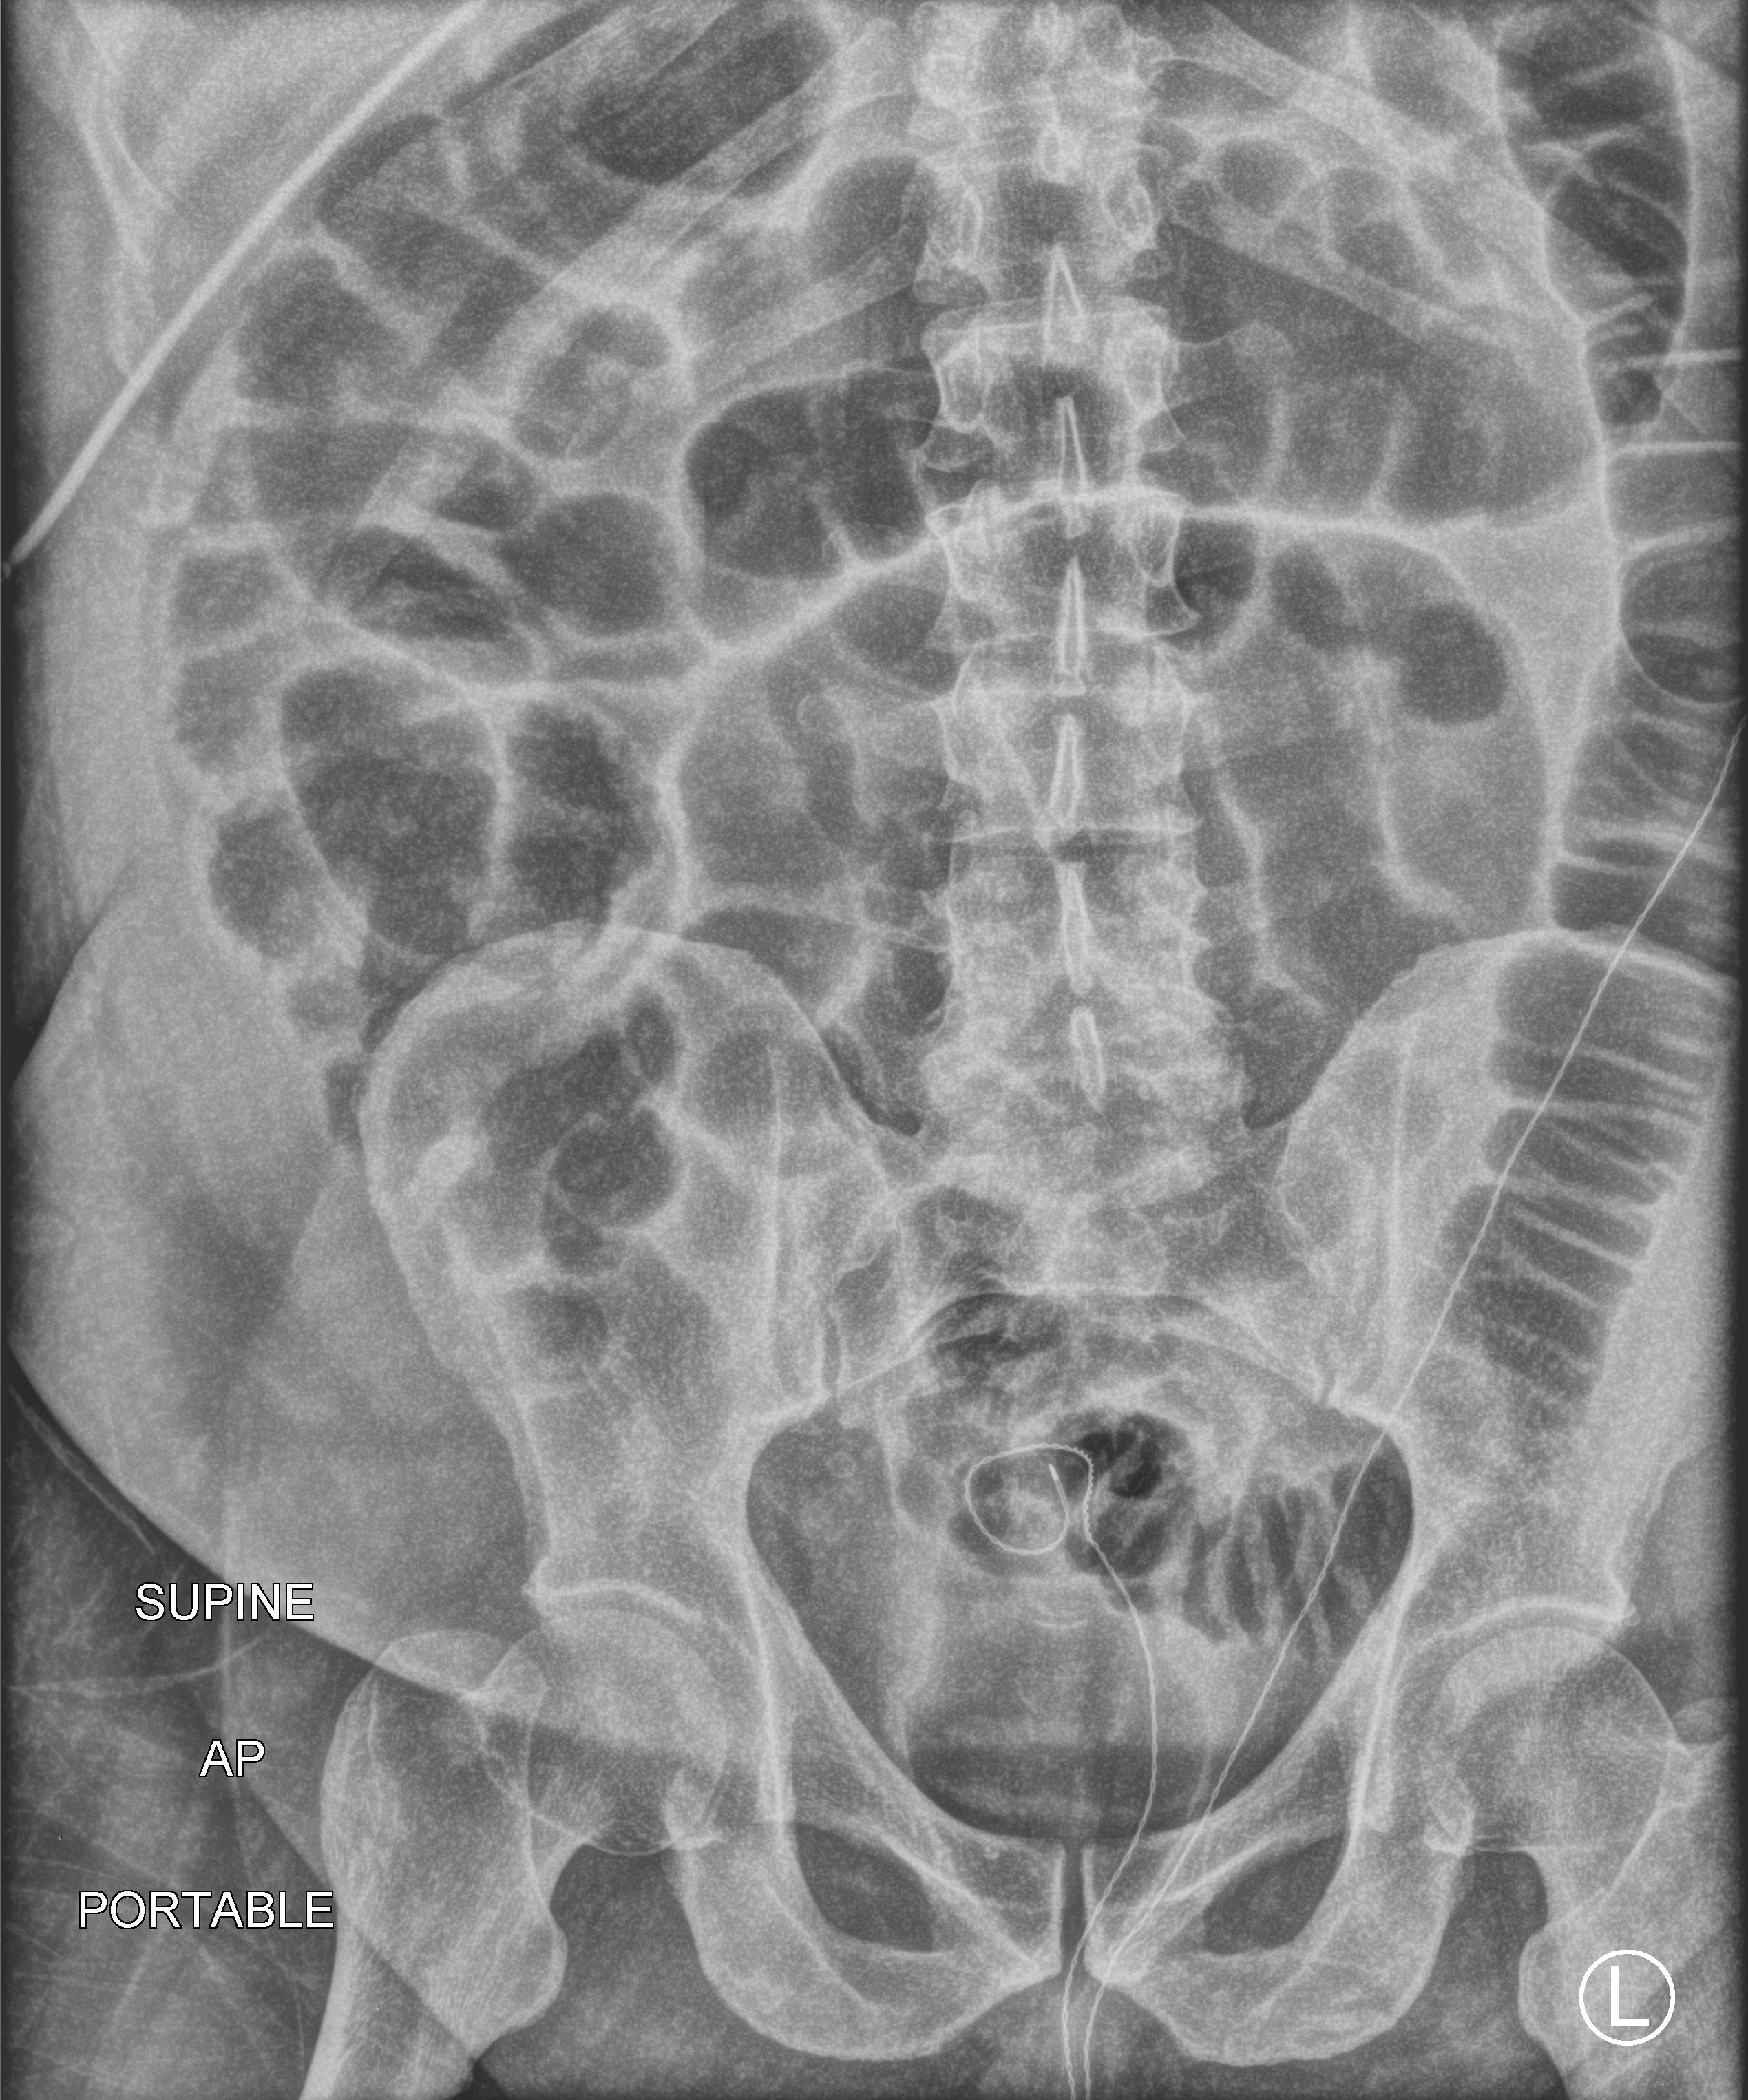
Abdomen X-ray (portable); anteroposterior (AP) projection. Male patient hospitalised with COVID-19, age 18–59 years.
Admission-level facts for this patient (not findings on this image; timing relative to this image not recorded): admitted to intensive care during this hospital stay: yes; smoking status (admission record): never.